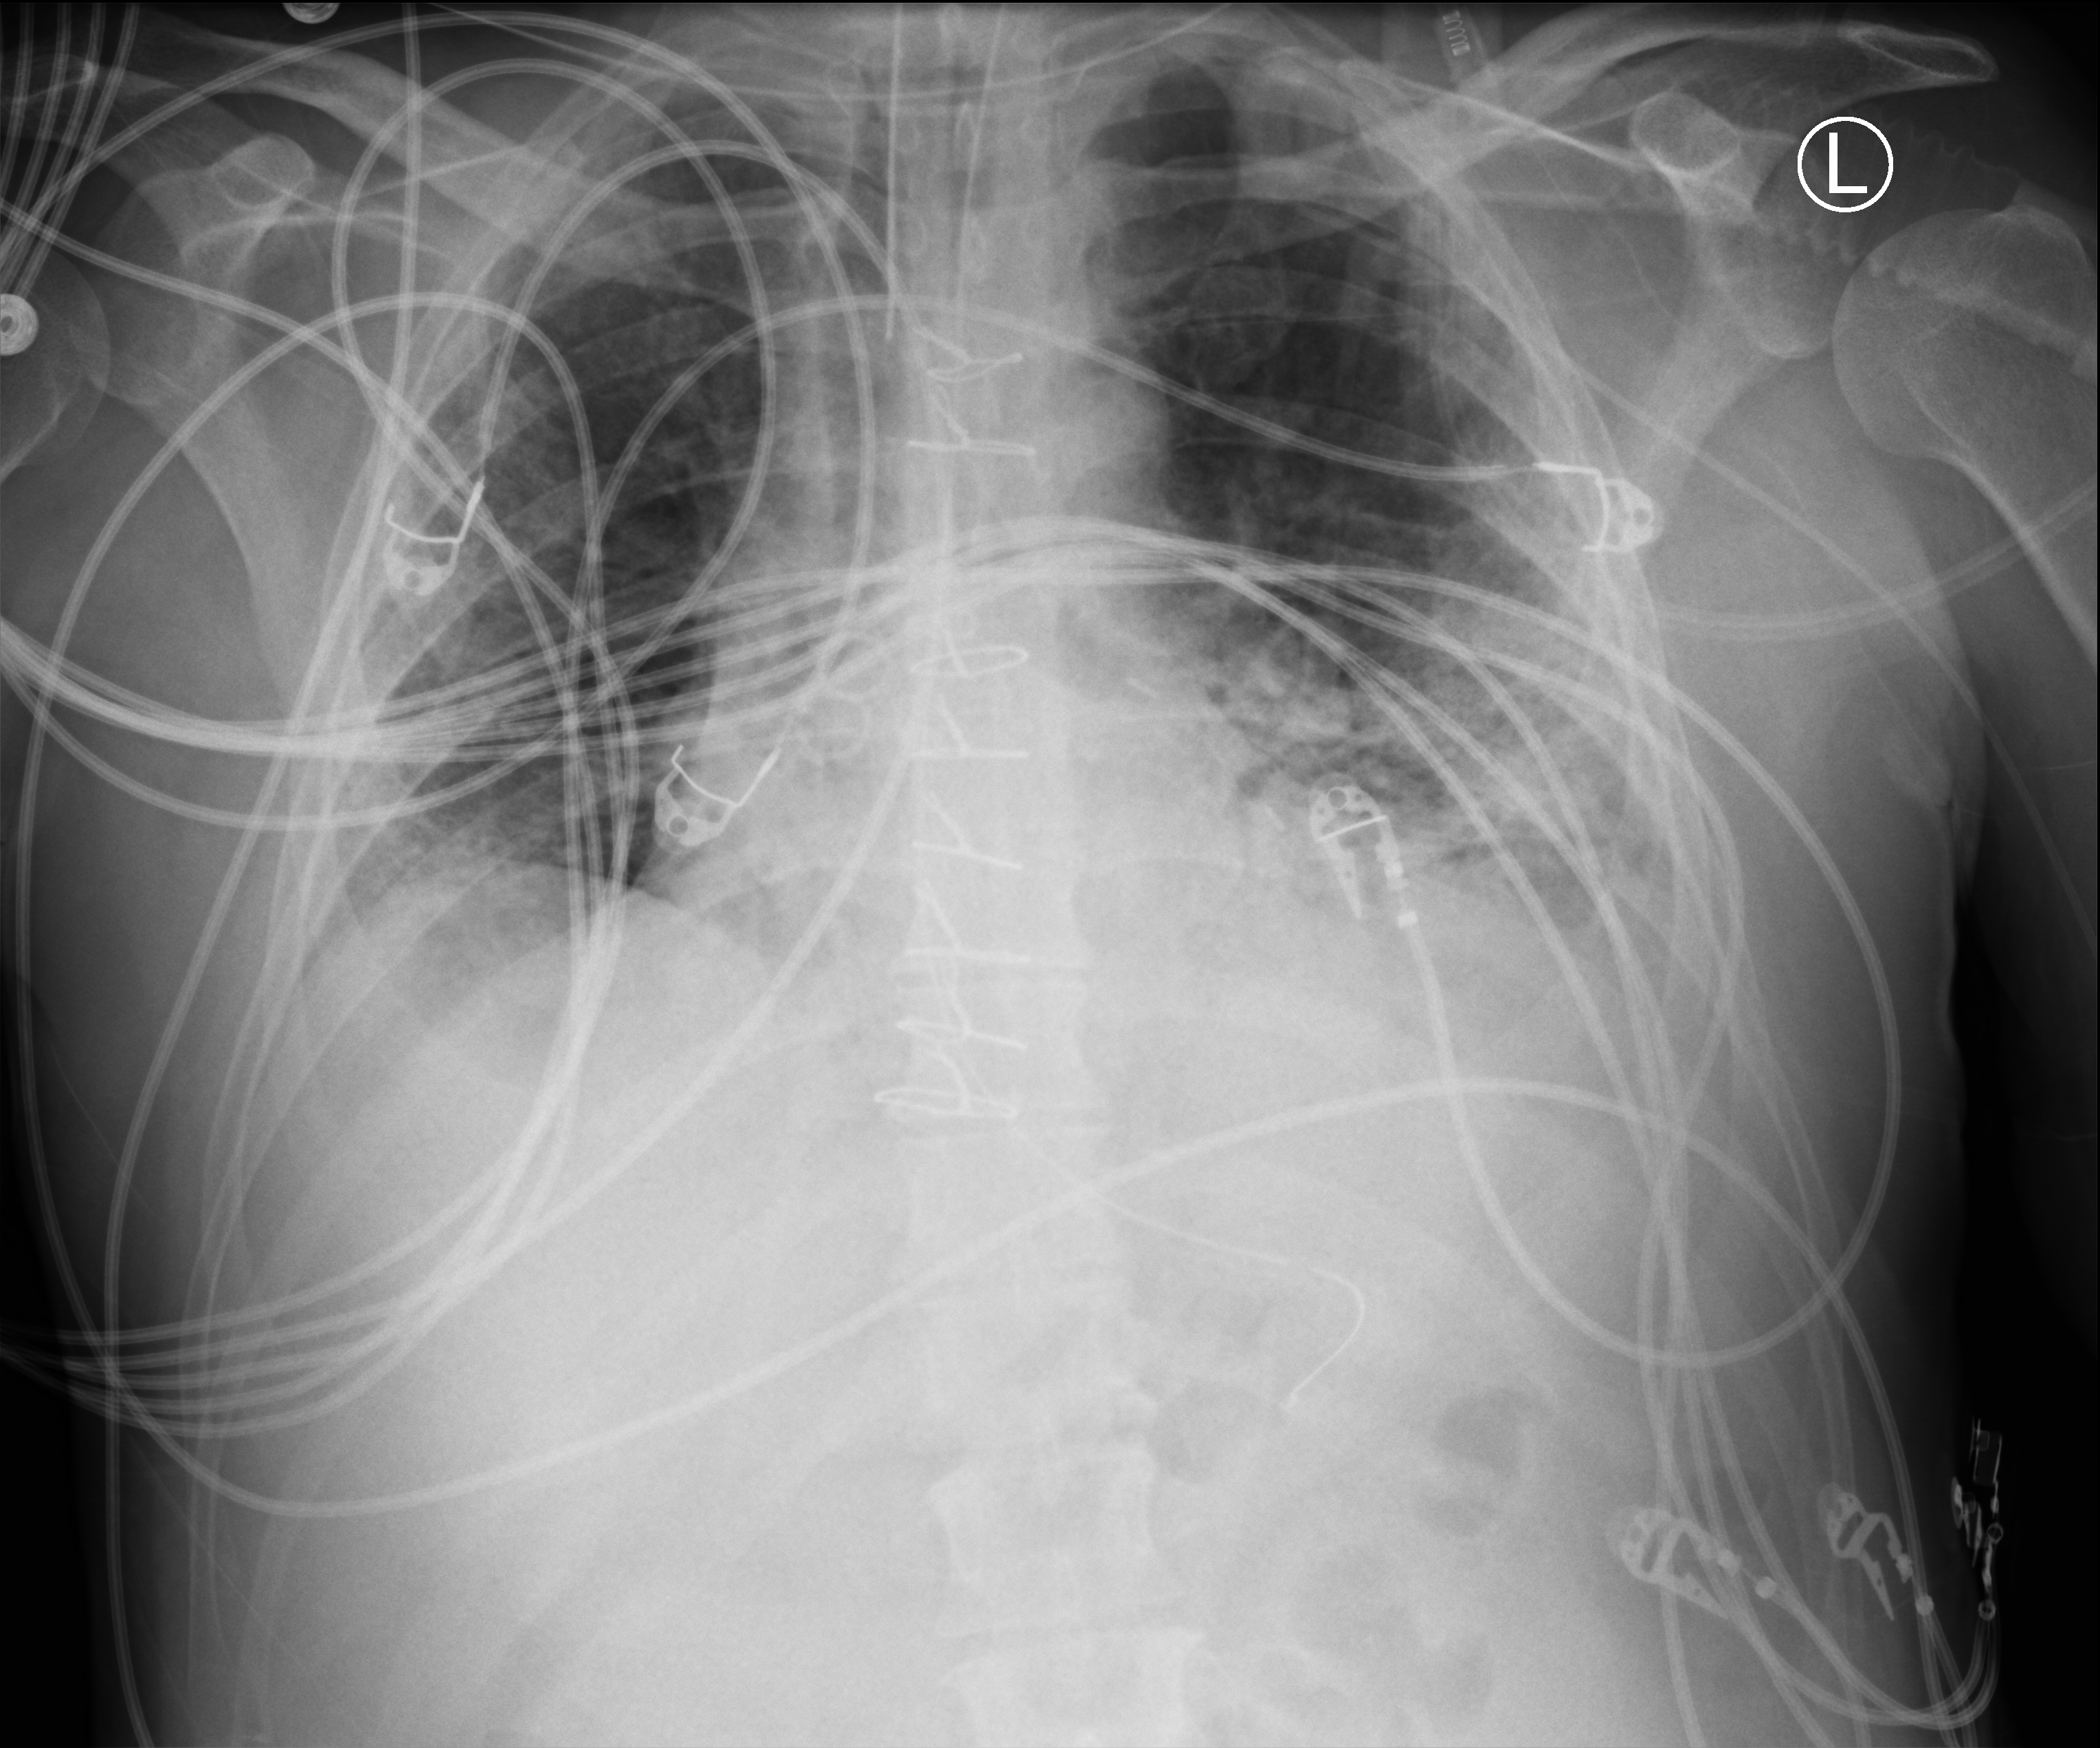
Bedside chest radiograph (computed radiography), anteroposterior (AP) projection. Patient hospitalised with COVID-19; male, aged 18–59 years.
Admission-level facts for this patient (not findings on this image; timing relative to this image not recorded):
- admitted to intensive care during this hospital stay: yes